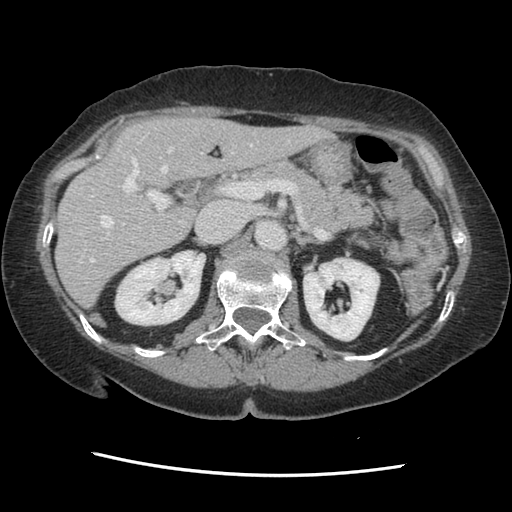
Contrast-enhanced abdominal CT, one axial slice. Position 81 of 141 along the scan axis. 120 kVp. Soft-tissue window (W 400 / L 40 HU). 2.5 mm slice thickness. 512 × 512 image matrix, field of view 330 × 330 mm. Female patient, age 61 years. Case-level facts recorded for this patient, not image findings: diagnosis: colorectal cancer liver metastases, imaged before liver resection; multiple liver metastases: no; largest metastasis: 2.4 cm.
Structures marked on this image (manually delineated by an expert):
- hepatic veins: bounding box [x1, y1, x2, y2] px = [90, 140, 289, 262]
- liver: [57, 118, 324, 306]
- planned liver remnant (the part of the liver to remain after resection): [57, 118, 324, 306]
- portal vein (with intrahepatic branches): [92, 158, 169, 210]